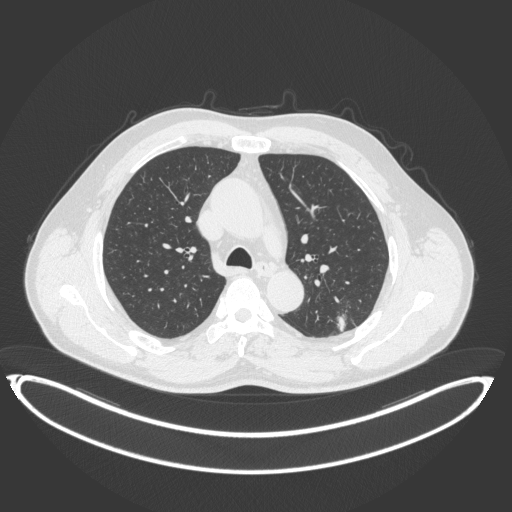
Chest CT, one axial slice. Position 243 of 399 along the scan axis. Reconstruction kernel B31f. 120 kVp. Lung window (W 1500 / L -600 HU). 1 mm slice thickness. 512 × 512 image matrix, field of view 469 × 469 mm. Male patient, age 58 years. From the clinical record (not read from this slice): clinical TNM (as recorded): T1c N0 M0; histopathological grade: G1-2.
Annotated regions visible in this slice (bounding box drawn by a radiologist):
- lung tumour (recorded histology: adenocarcinoma): bounding box (x1, y1, x2, y2) in pixels: (331, 305, 359, 336)